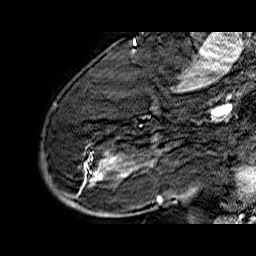
Breast MRI (dynamic contrast-enhanced), one sagittal slice. Slice 45 of 60 in the series (ordered by position). Dynamic contrast-enhanced series, time point 2 of 6 at this slice position (early post-contrast). 1.5 T. TE 6.5 ms, TR 32.9 ms. 4 mm slice thickness. 256 × 256 image matrix, field of view 200 × 200 mm. Female patient. From the clinical record (not read from this slice): setting: breast cancer imaged before/during neoadjuvant chemotherapy; receptor status: HR-positive, HER2-negative.
Outlined on this slice (semi-automatically segmented with operator editing):
- analysis volume of interest (the breast-tissue region the enhancement analysis was run in; not a lesion): bounding box (x1, y1, x2, y2) in pixels: (41, 74, 176, 210)
- tumour enhancement mask (voxels above the 100 % enhancement threshold inside the analysis volume of interest): (84, 145, 162, 203)